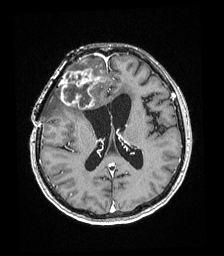
Brain MRI from a brain-tumour surgery series, one axial slice. T1-weighted post-contrast. 1 mm slice thickness. 224 × 256 image matrix. Case-level facts recorded for this patient, not image findings: histopathology: Astrocytoma; WHO grade: 4; IDH mutation: yes.
Annotated regions visible in this slice (outlined manually by an expert reader):
- tumour: bounding box <61,68,104,109> (left, top, right, bottom; pixels)